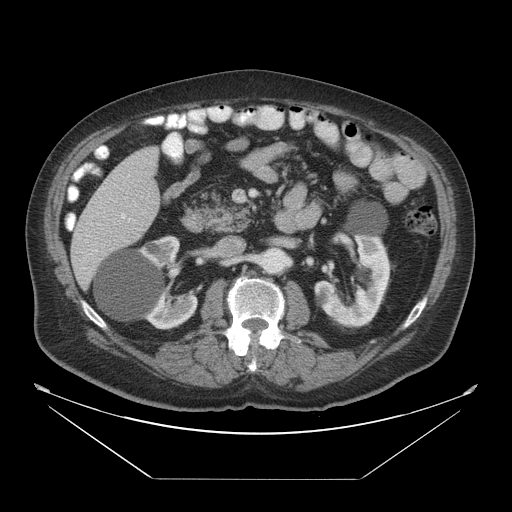
Contrast-enhanced abdominal CT, one axial slice. Reconstruction kernel STANDARD. 120 kVp. Intravenous contrast given. Soft-tissue window (W 400 / L 40 HU). 5 mm slice thickness. 512 × 512 image matrix, field of view 463 × 463 mm. Male patient, age 87 years. Case-level facts recorded for this patient, not image findings: diagnosis: colorectal cancer liver metastases, imaged before liver resection; multiple liver metastases: no; largest metastasis: 4.5 cm; disease in both lobes: yes.
Annotated regions visible in this slice (manually delineated by an expert):
- liver: bounding box (x1, y1, x2, y2) in pixels: (70, 146, 162, 291)
- portal vein (with intrahepatic branches): (121, 213, 135, 223)